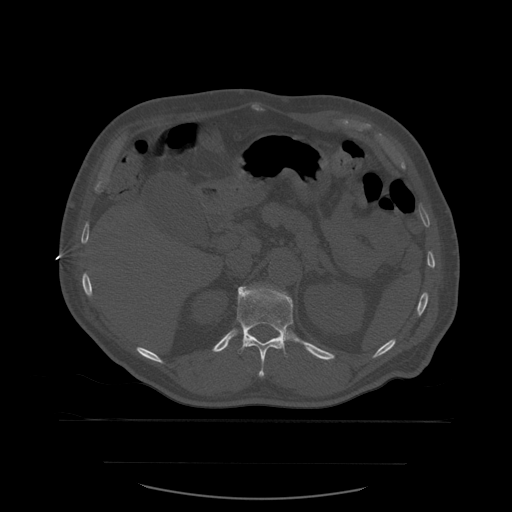
CT including the spine, one axial slice. Position 270 of 590 along the scan axis. Bone window (W 1800 / L 400 HU). 1.25 mm slice thickness. 512 × 512 image matrix, field of view 479 × 479 mm. Patient age 71 years. From the clinical record (not read from this slice): primary cancer: lung.
Outlined on this slice (semi-automatic segmentation, software-assisted and operator-edited):
- T12 vertebra: box from (x=237, y=286) to (x=294, y=378) px